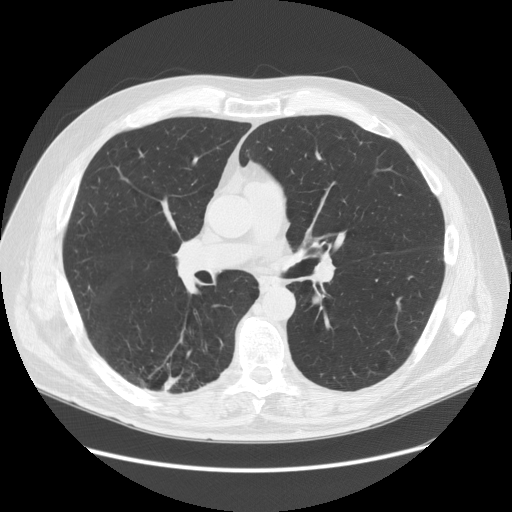
Low-dose screening chest CT, one axial slice; position 80 of 149 along the scan axis; lung window (W 1500 / L -600 HU); 512 × 512 image matrix.
Annotated regions visible in this slice (outlined manually by an expert reader):
- lesion 1 (tumor, lower lobe of right lung): bounding box (x1, y1, x2, y2) in pixels: (163, 375, 180, 392)